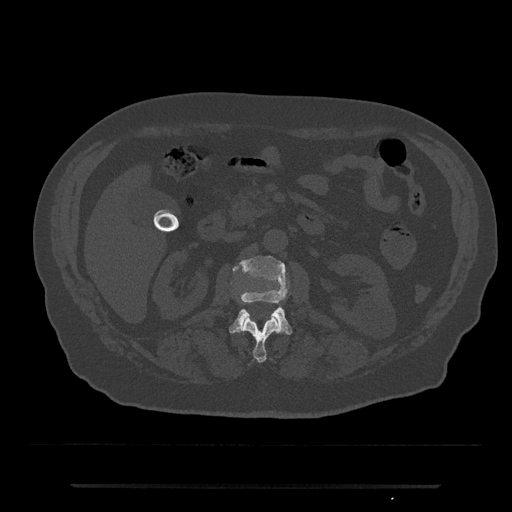
CT including the spine, one axial slice; position 501 of 797 along the scan axis; reconstruction kernel Br40s/3; 120 kVp; bone window (W 1800 / L 400 HU); 0.5 mm slice thickness; 512 × 512 image matrix, field of view 434 × 434 mm. Patient: male, 80 years. From the clinical record (not read from this slice): primary cancer: prostate; vertebrae with lytic lesions (as recorded): L1, T11.
Annotated regions visible in this slice (semi-automatically segmented with operator editing):
- L1 vertebra: bounding box <243,317,280,363> (left, top, right, bottom; pixels)
- L2 vertebra: <229,256,292,335>